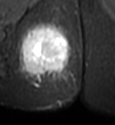
MRI of an extremity soft-tissue mass, one axial slice; slice 20 of 49 in the series (ordered by position); STIR; MR volume resampled by the dataset authors to the PET/CT grid (not the native acquisition matrix); 3.27 mm slice thickness; 115 × 125 image matrix, field of view 112 × 122 mm. Female patient. From the clinical record (not read from this slice): histological type: epithelioid sarcoma; grade: intermediate; site of the primary tumour: right buttock.
Outlined on this slice (expert contour drawn on MRI and transferred to this co-registered scan by the dataset authors):
- gross tumour volume including surrounding oedema: box from (x=15, y=19) to (x=73, y=86) px
- gross tumour volume (mass): (x=20, y=25)–(x=71, y=76)